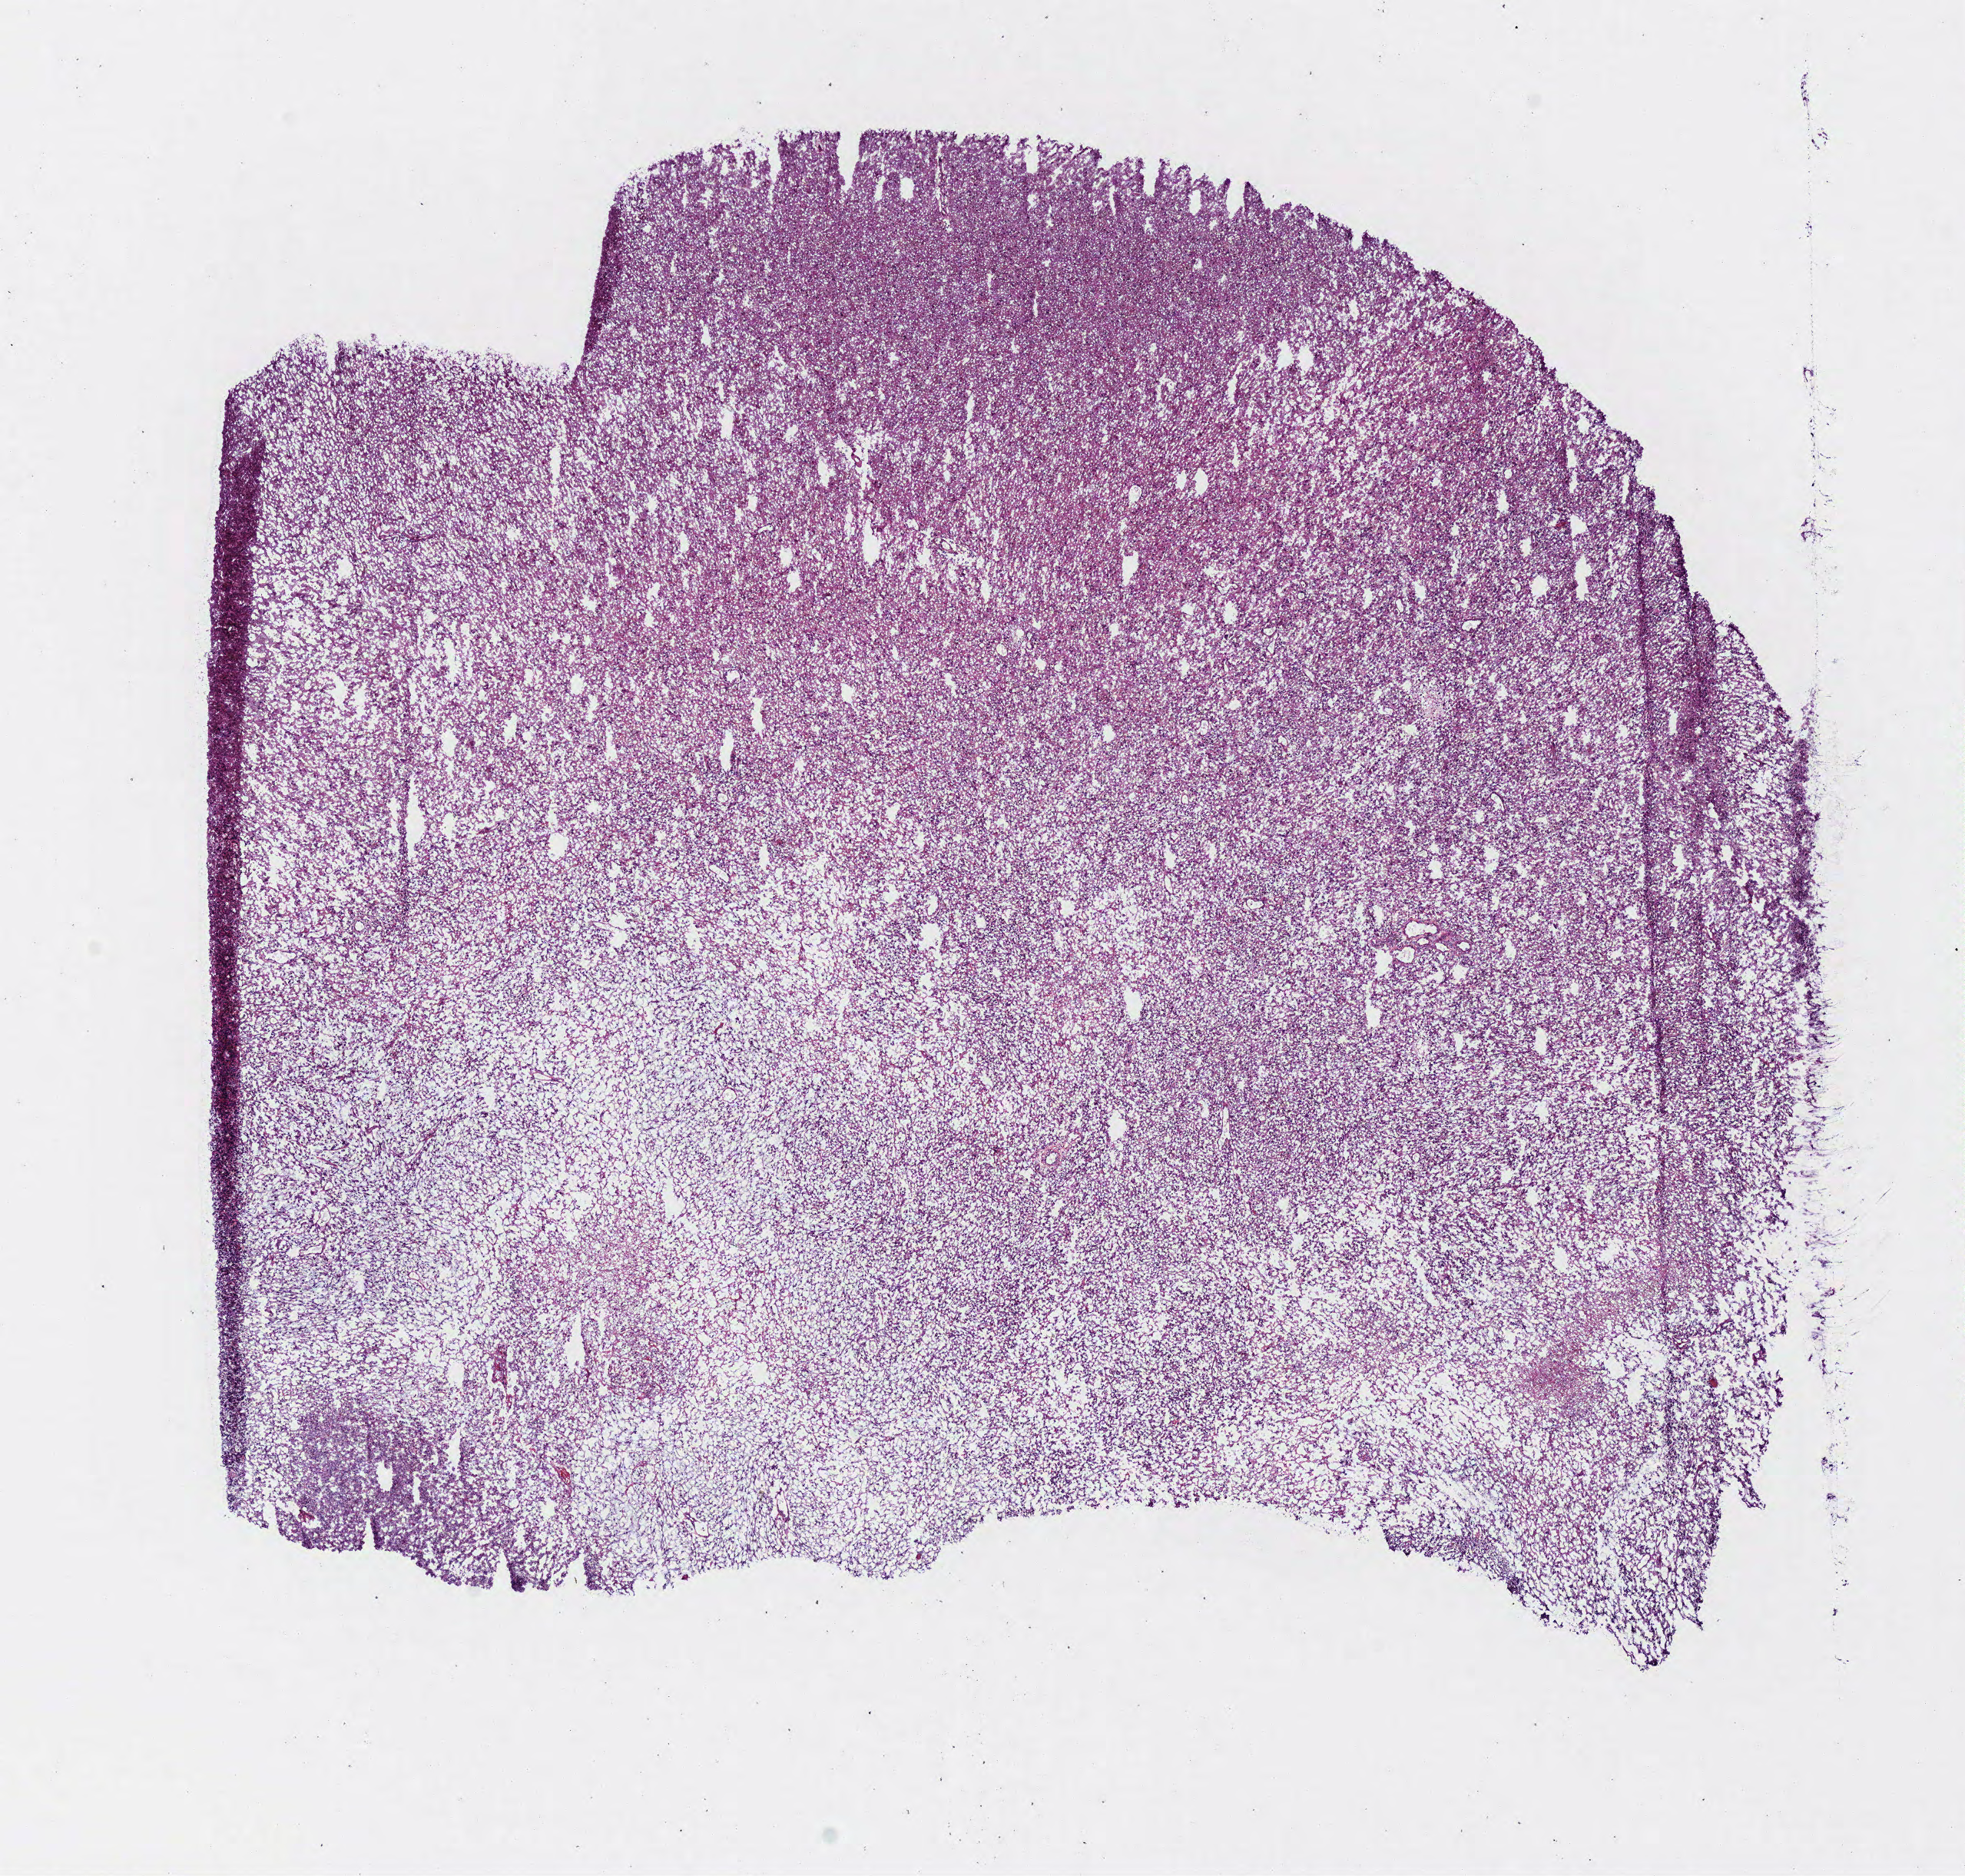
Digitized H&E tissue section (whole slide), shown as a low-resolution overview of the whole scanned area (about 10.1 x 9.6 mm, from a 40x scan), frozen section, brain, primary tumour sample. Male, age 83 years at initial diagnosis. Slide review estimates, as recorded: tumour cells 100%, tumour nuclei 70%, normal cells 0%, stromal cells 0%, necrosis 0%.
Diagnosis: Glioblastoma.